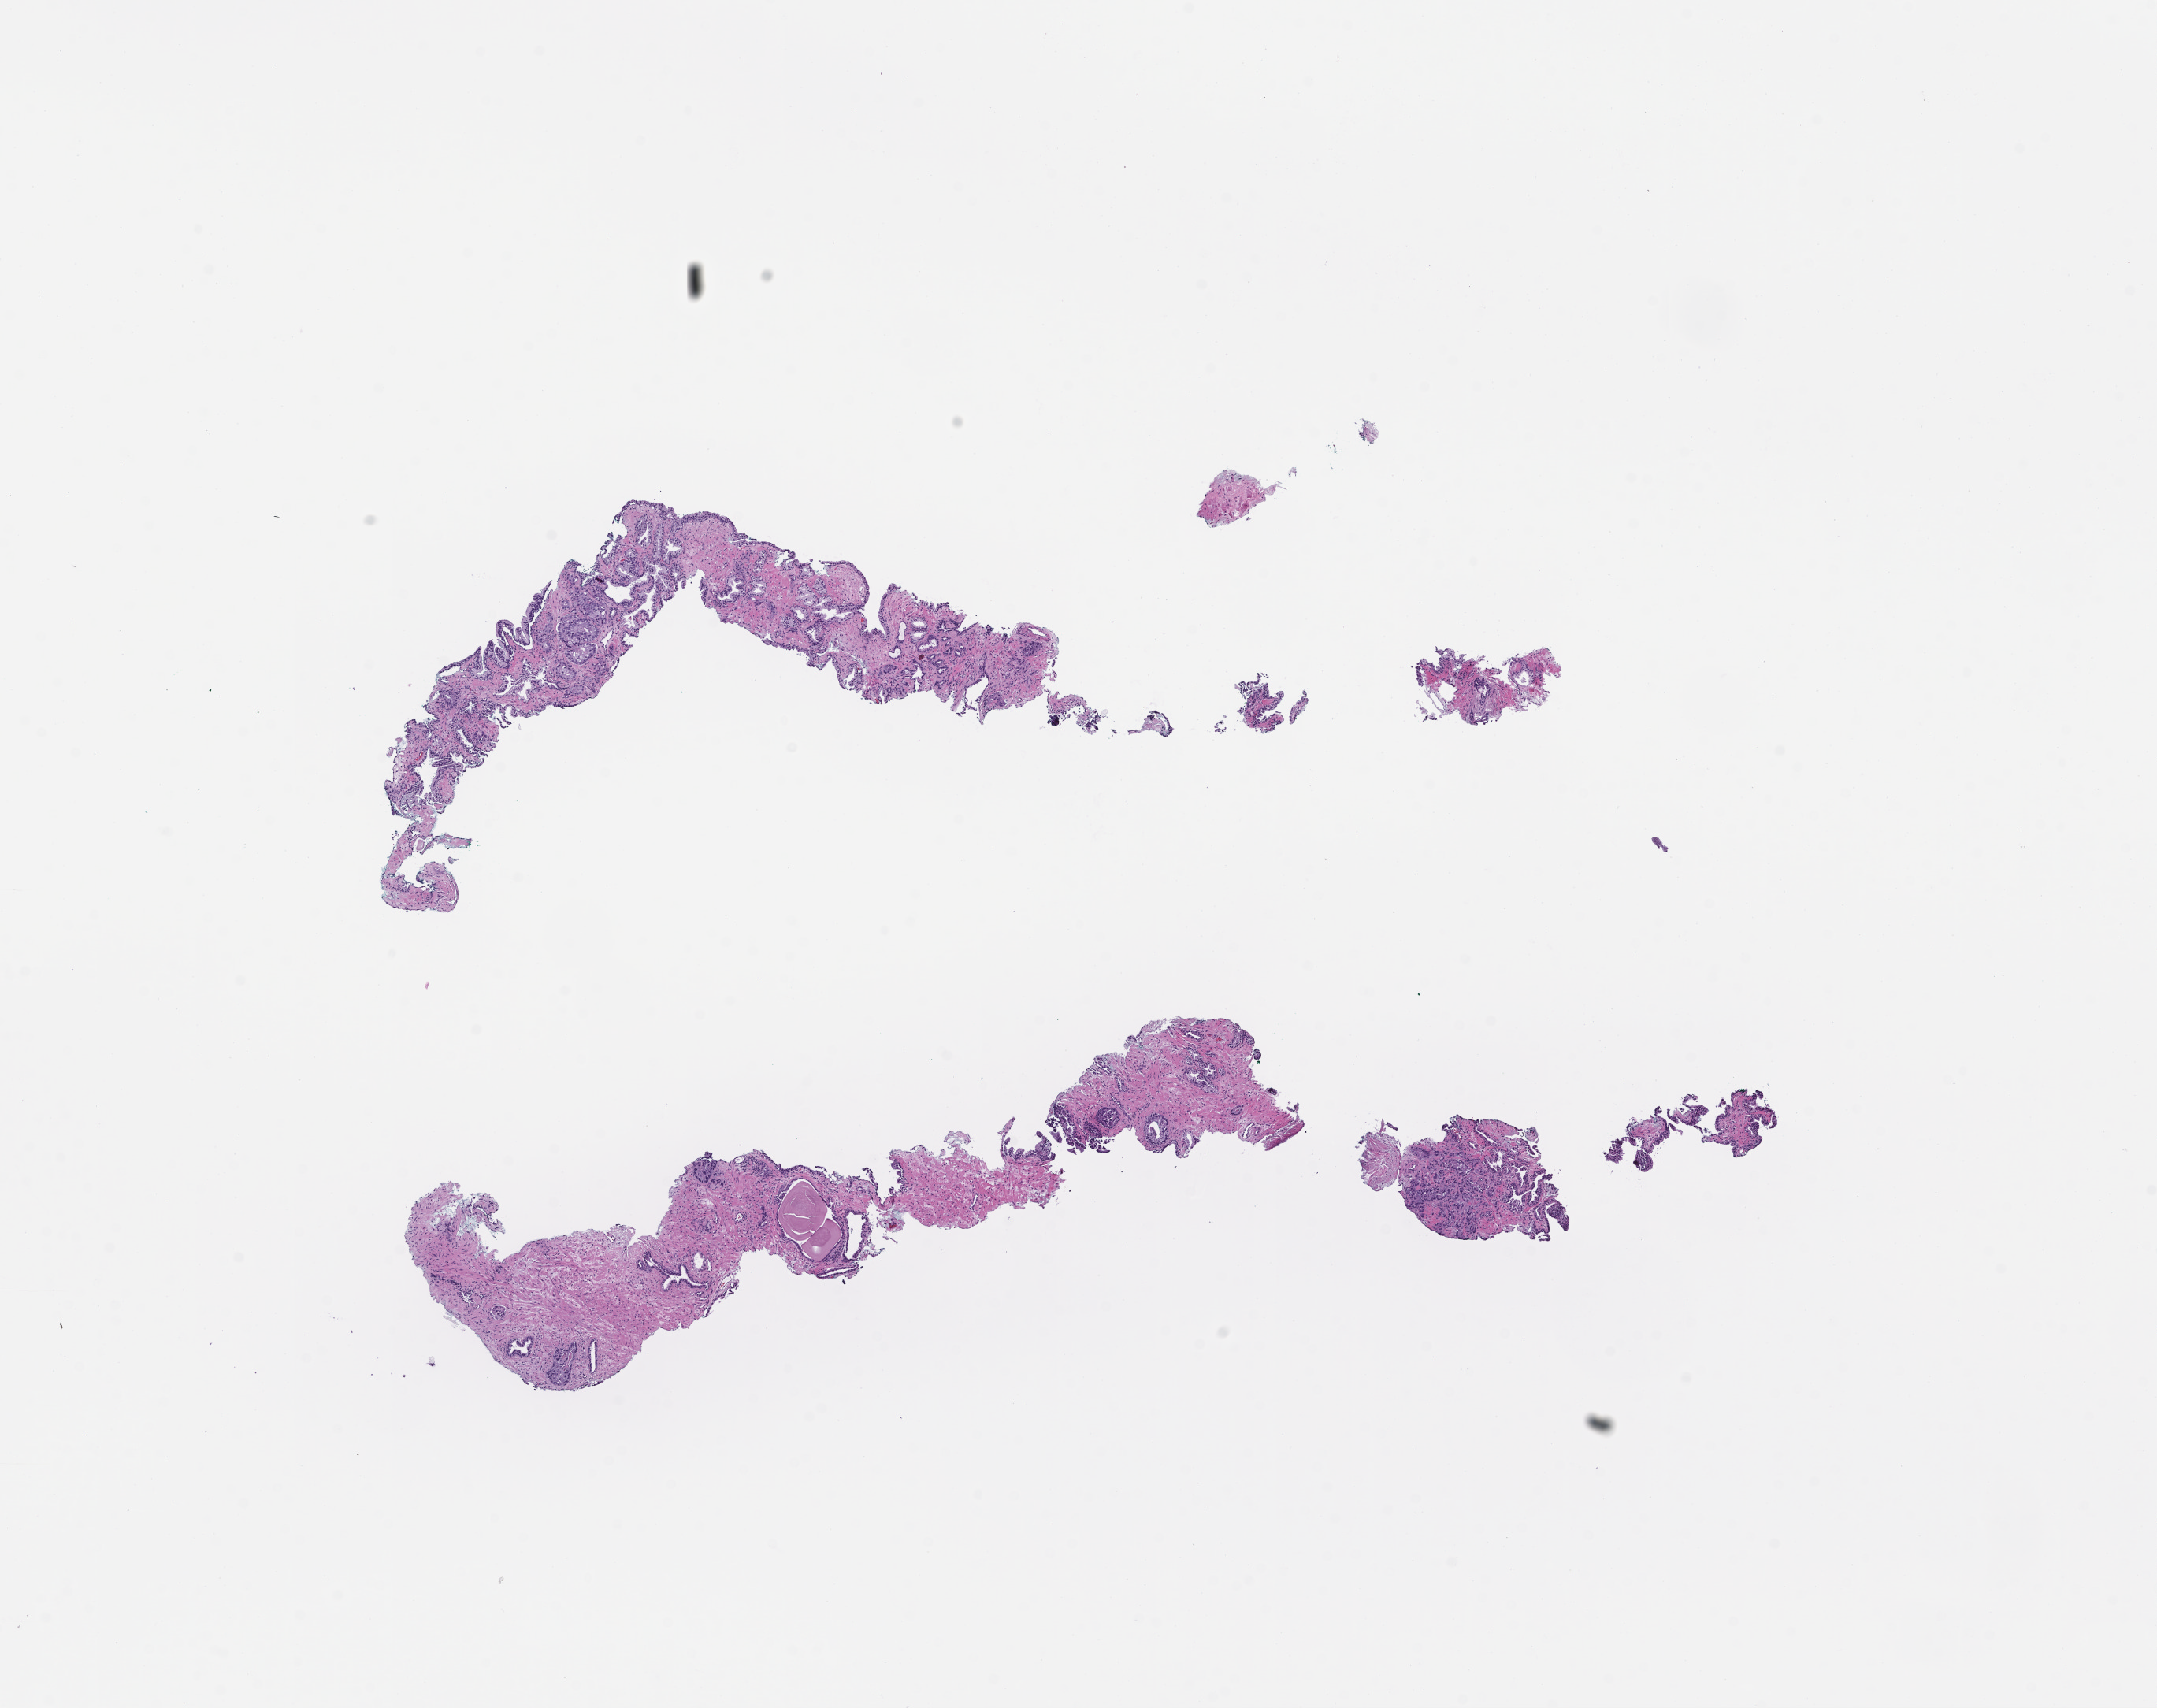
H&E whole-slide image — low-resolution overview of the scanned area, about 11.1 x 8.8 mm, FFPE section, site: prostate, archival tissue. Patient sex: male.
This section: primary tumor. Diagnosis: Prostate Carcinoma.